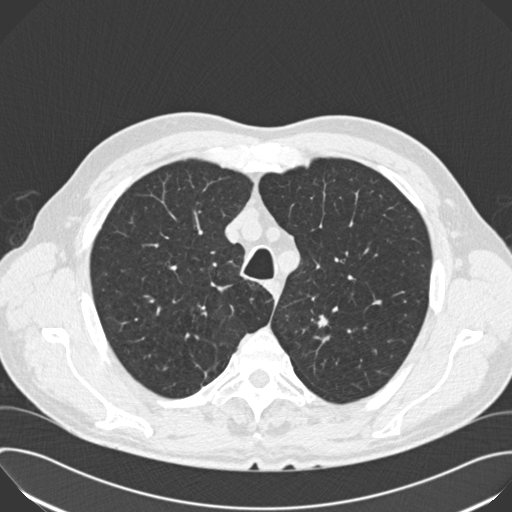
Axial slice from a low-dose chest CT screening exam; second annual screen; lung window (W 1500 / L -600 HU); standard (soft-tissue) reconstruction kernel (B30f); 512 × 512 image matrix. Male participant, aged 66 years at enrolment. Current smoker at enrolment.
Expert-annotated lung lesion, bounding box <304,302,344,341> (left, top, right, bottom; pixels). Reader record for this screening exam (exam-level; its link to the box is not recorded): non-calcified nodule or mass ≥4 mm, left upper lobe, 8 × 7 mm, poorly defined margins, soft tissue attenuation, pre-existing on the prior screen: yes; interval growth: yes. Official screen result: positive, other.